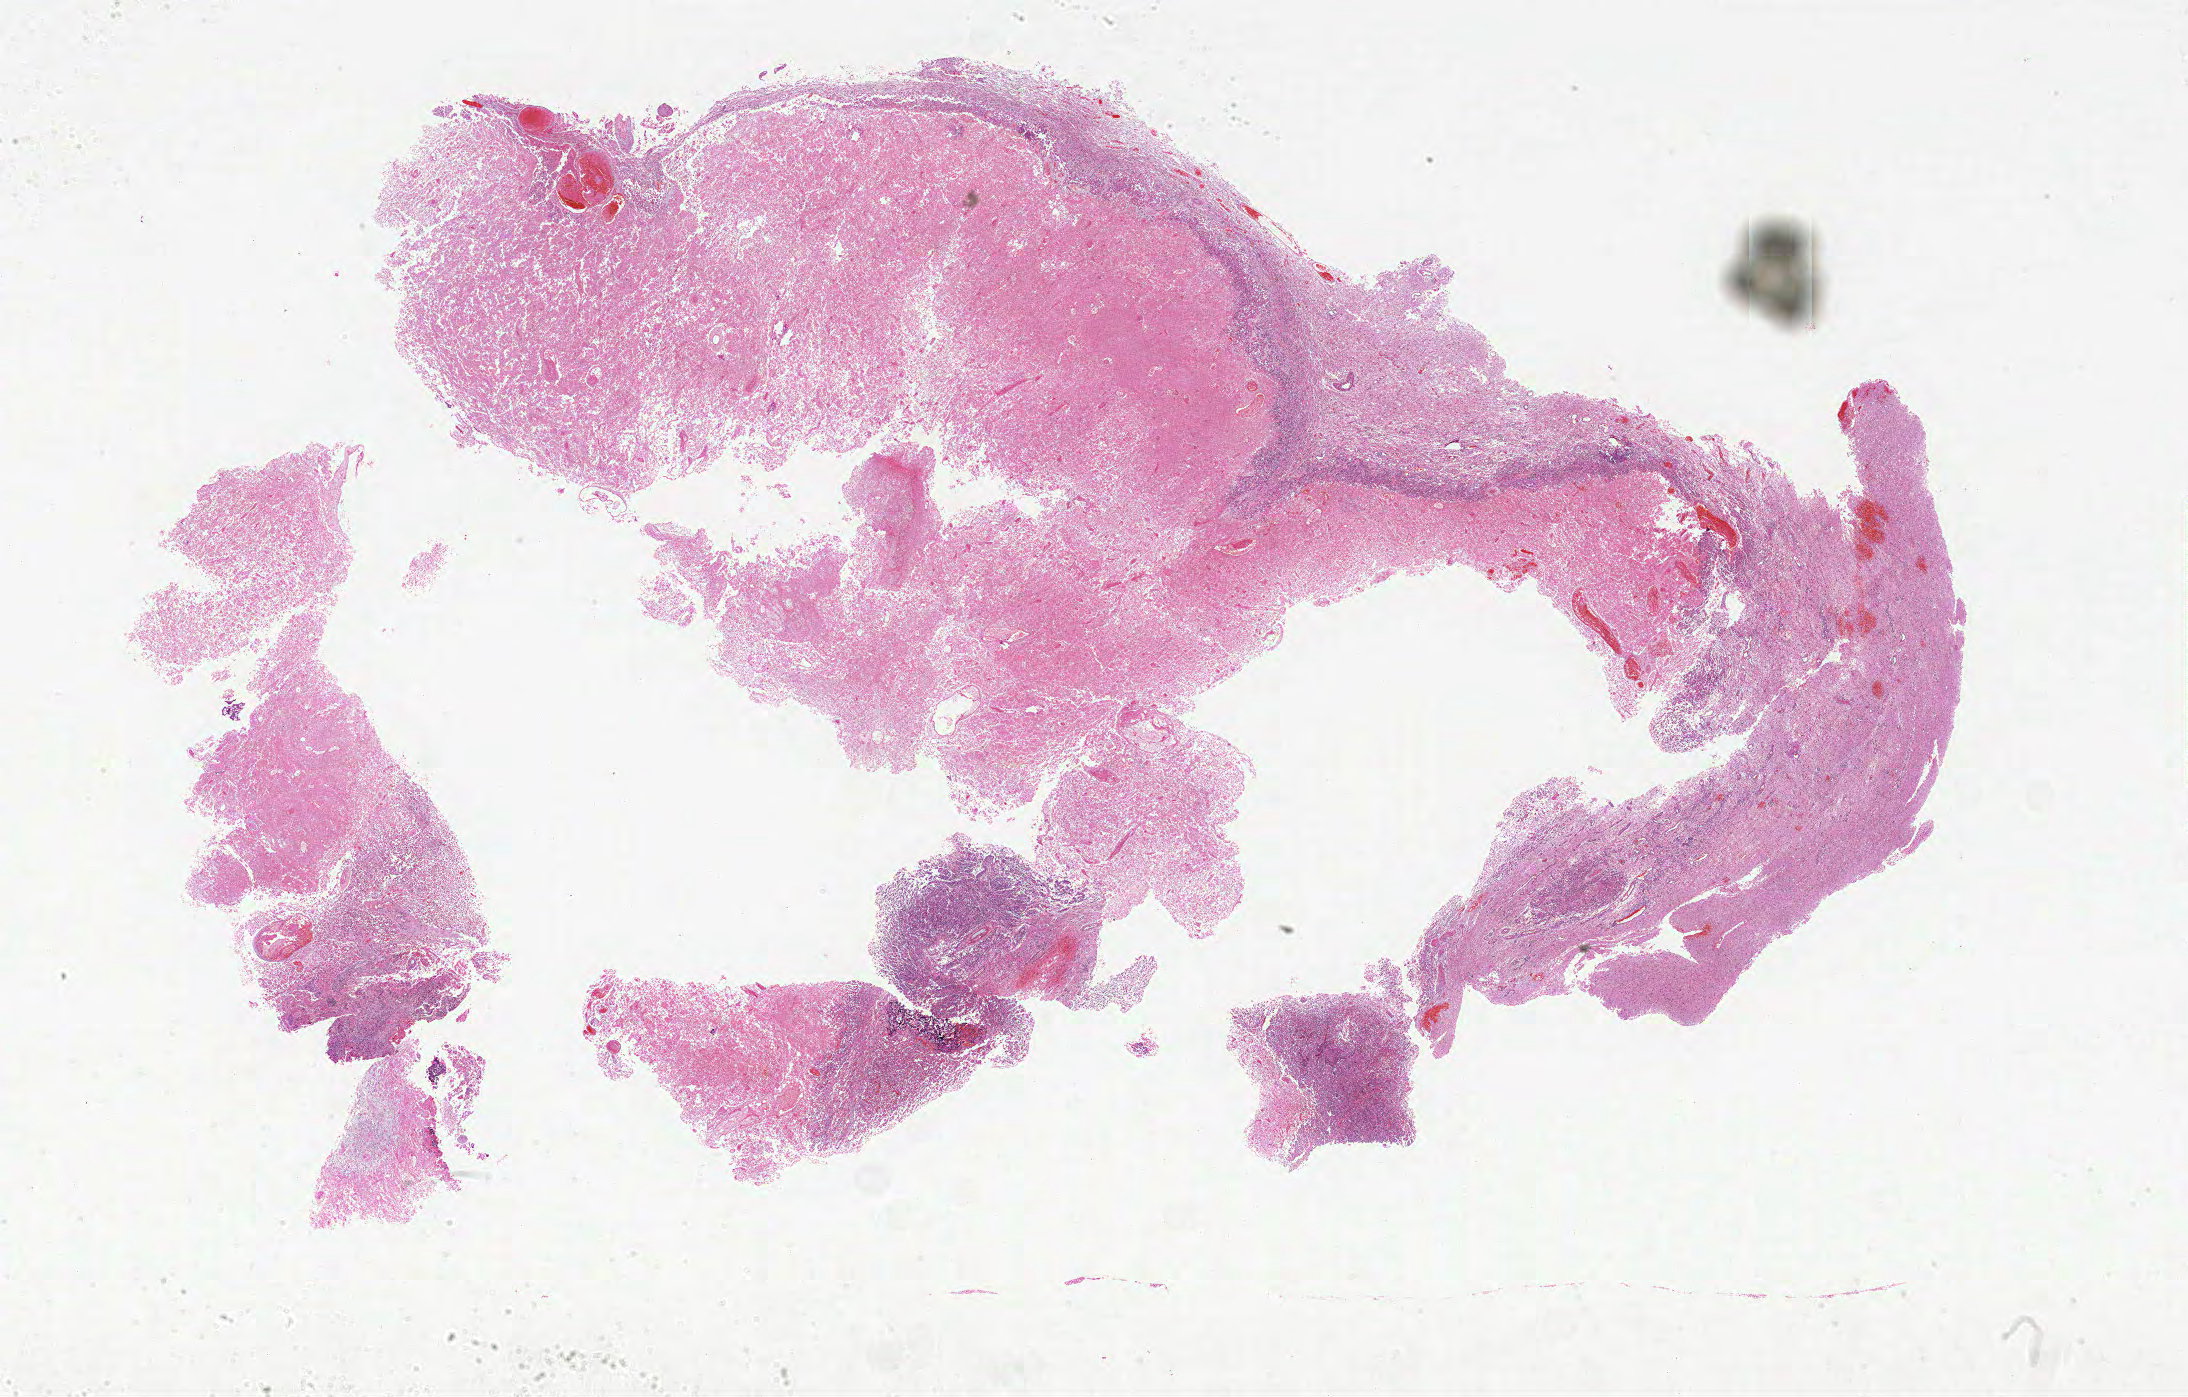
H&E-stained whole-slide image — a low-resolution overview of the entire scanned area, about 35.0 x 22.3 mm; formalin-fixed paraffin-embedded (FFPE) diagnostic section; primary tumour sample from the brain. Male, age 64 years at initial diagnosis.
Histologic diagnosis: Glioblastoma.